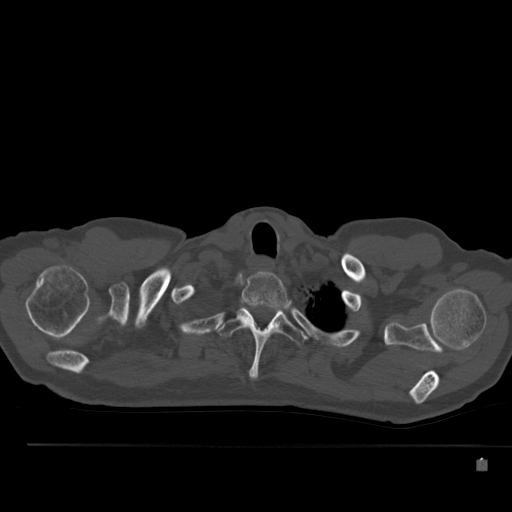
CT including the spine, one axial slice; reconstruction kernel Br40s; 120 kVp; bone window (W 1800 / L 400 HU); 1.5 mm slice thickness; 512 × 512 image matrix, field of view 408 × 408 mm. Male patient, age 70 years. Case-level facts recorded for this patient, not image findings: primary cancer: renal; vertebrae with lytic lesions (as recorded): T4, T6, T10, T12, L3, L4, L5.
Outlined on this slice (semi-automatic segmentation, software-assisted and operator-edited):
- T1 vertebra: bounding box (x1, y1, x2, y2) in pixels: (241, 271, 288, 308)
- T2 vertebra: (217, 303, 308, 380)